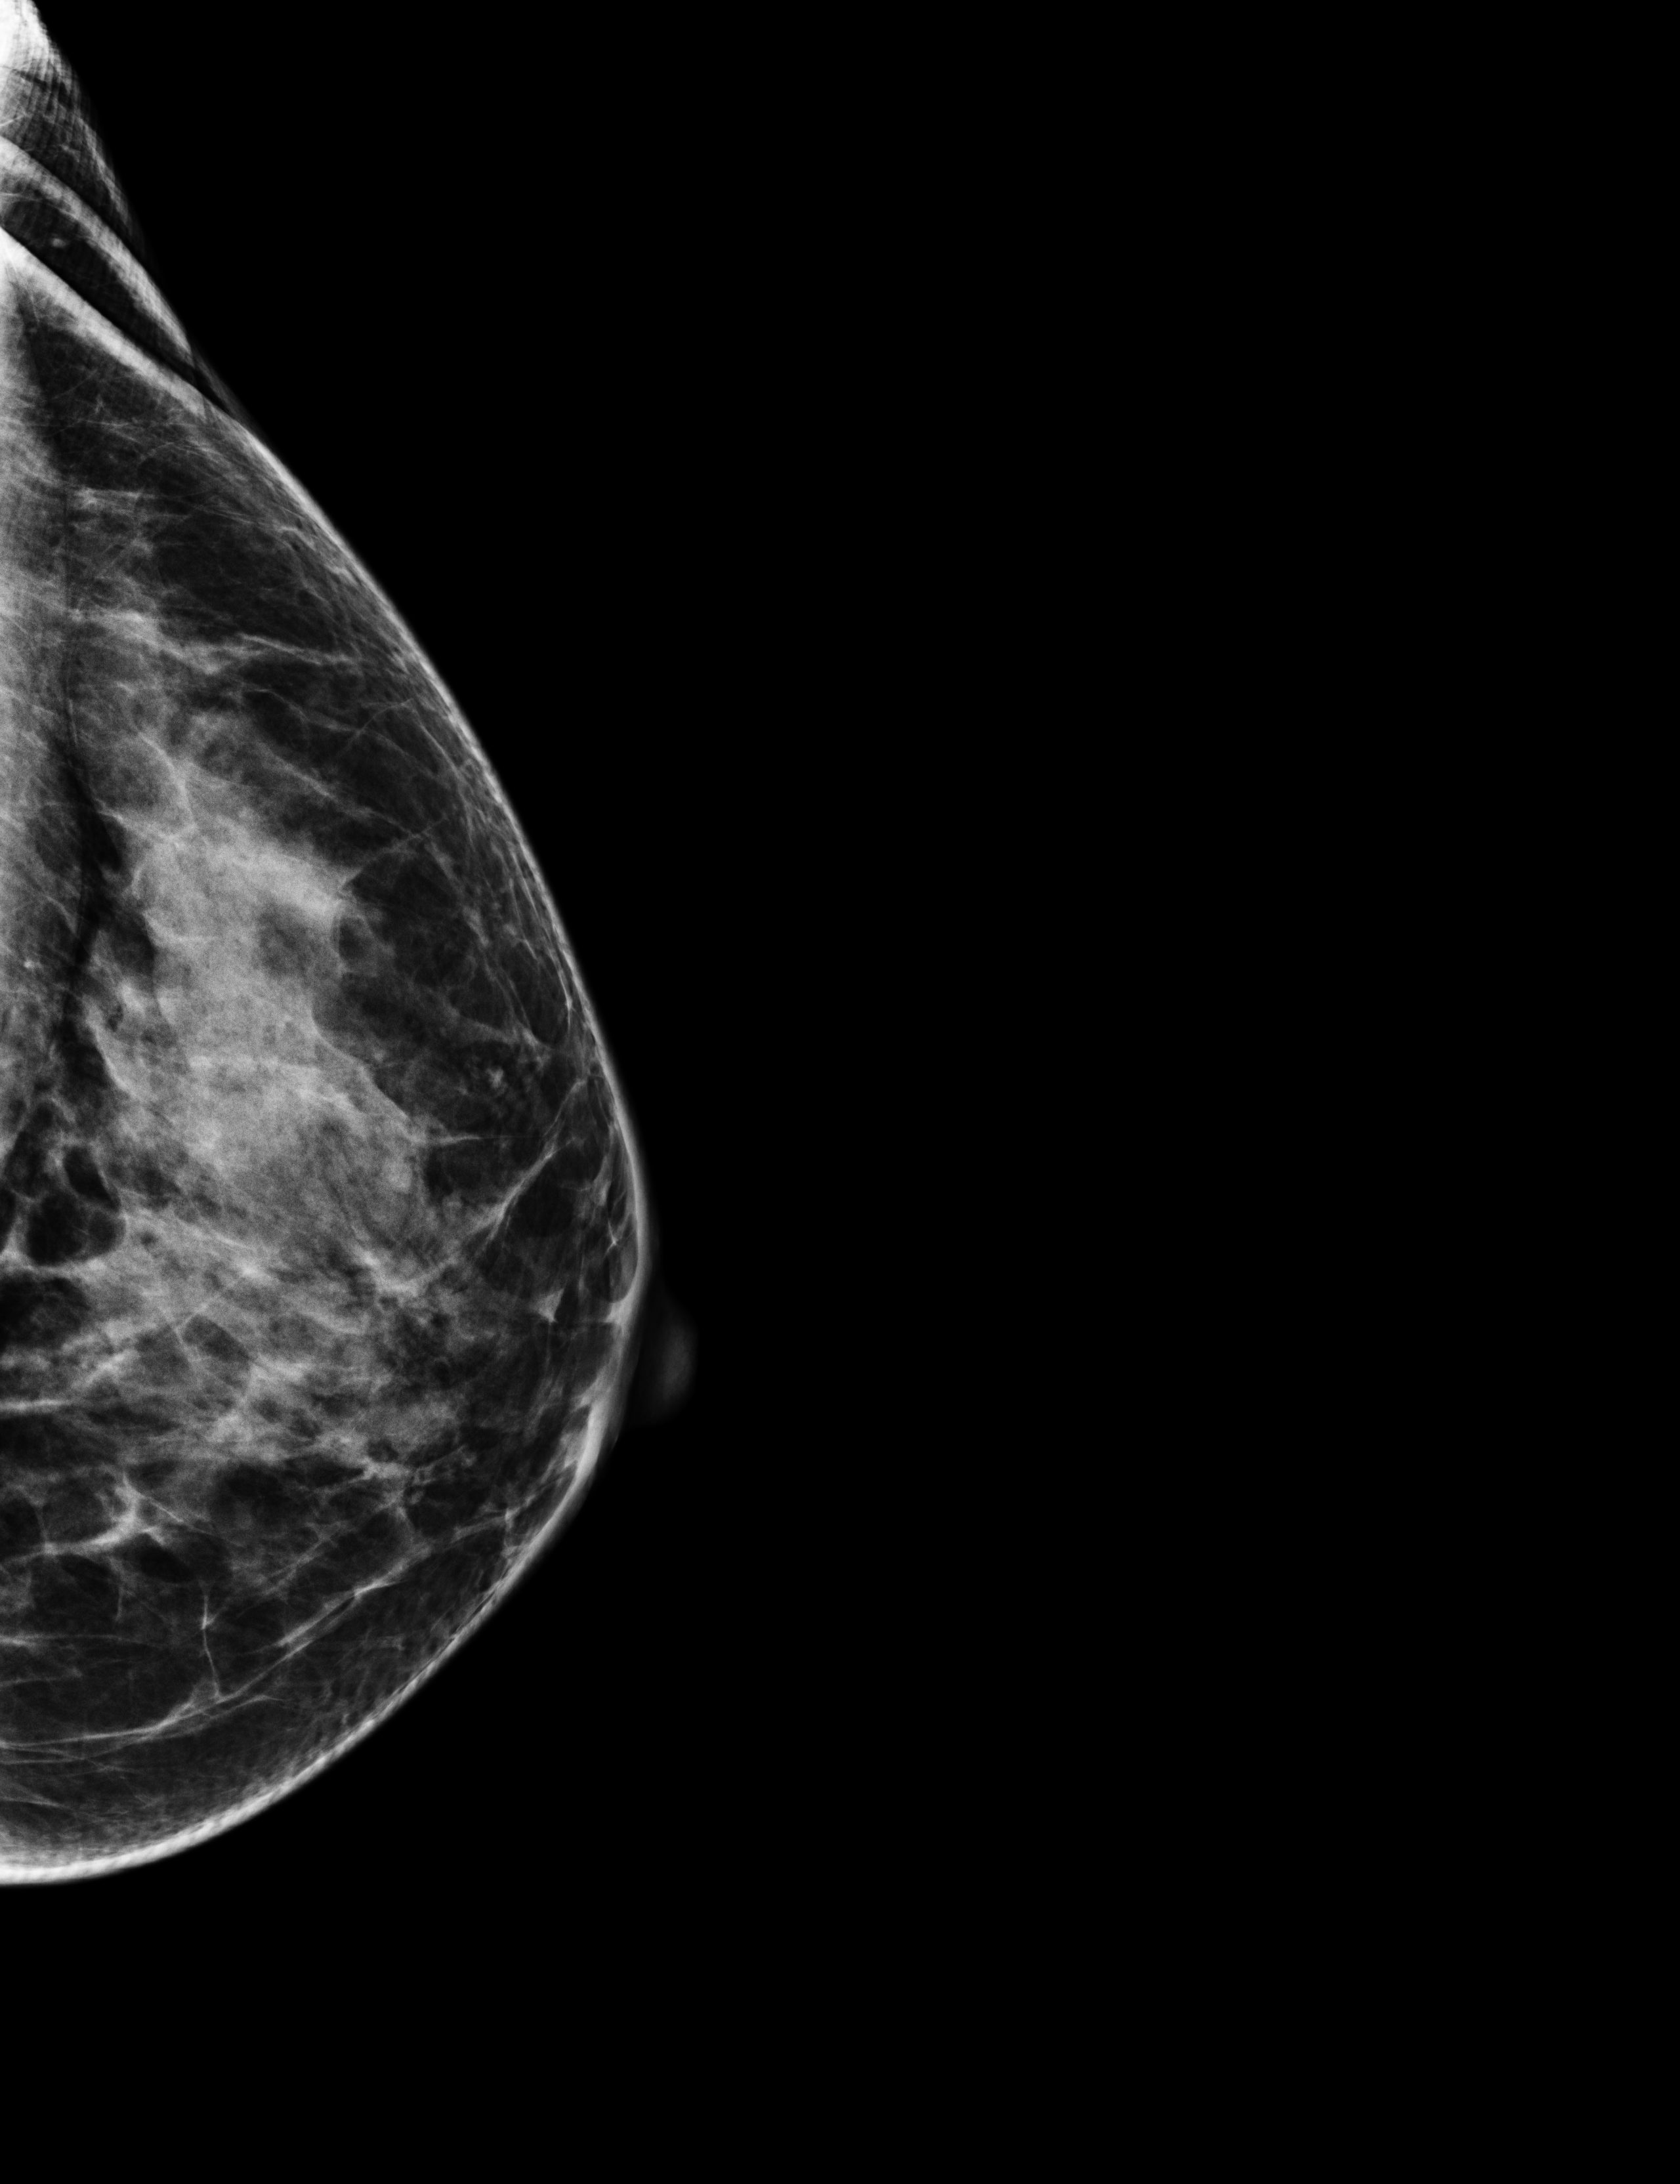
Screening examination. Female patient, age 53 years.
Image type: full-field digital mammogram. Breast: left. Projection: exaggerated CC view (lateral).